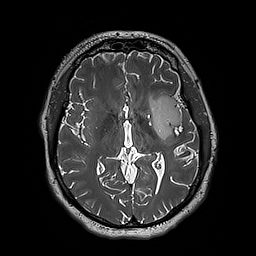
Brain MRI from a brain-tumour surgery series, one axial slice. Slice 105 of 192 in the series (ordered by position). 1 mm slice thickness. 256 × 256 image matrix, field of view 250 × 250 mm. From the clinical record (not read from this slice): histopathology: Astrocytoma; WHO grade: 3; IDH mutation: yes.
Structures marked on this image (outlined manually by an expert reader):
- tumour: bounding box (x1, y1, x2, y2) in pixels: (147, 95, 182, 140)